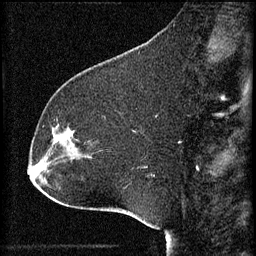
Breast MRI (dynamic contrast-enhanced), one sagittal slice. Position 20 of 60 along the scan axis. 3 images stored at this slice position (order not interpretable as contrast timing). 1.5 T. TE 4.2 ms, TR 8.2 ms. 2 mm slice thickness. 256 × 256 image matrix. Patient: female, 32 years.
Structures marked on this image (semi-automatic segmentation, software-assisted and operator-edited):
- analysis volume of interest (the breast-tissue region the enhancement analysis was run in; not a lesion): box from (x=47, y=118) to (x=84, y=157) px
- tumour enhancement mask (voxels above the 70 % enhancement threshold inside the analysis volume of interest): (x=61, y=140)–(x=63, y=143)